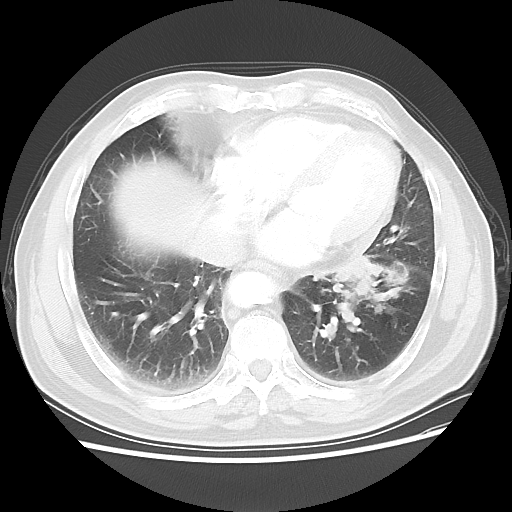
Chest CT, one axial slice; lung window (W 1500 / L -600 HU); 5 mm slice thickness; 512 × 512 image matrix. Patient: male, 75 years. From the clinical record (not read from this slice): clinical TNM (as recorded): T3 N0 M0.
Structures marked on this image (rectangle marked by the reading radiologist):
- lung tumour (recorded histology: squamous cell carcinoma): box from (x=333, y=248) to (x=386, y=302) px